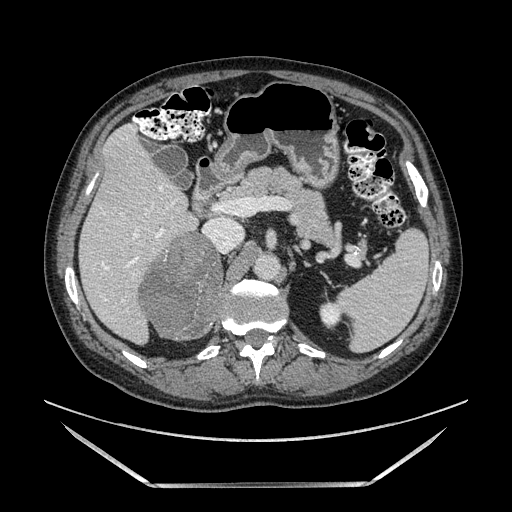
Contrast-enhanced abdominal CT, one axial slice; position 84 of 185 along the scan axis; soft-tissue window (W 400 / L 40 HU); 1.25 mm slice thickness; 512 × 512 image matrix. Male patient. Case-level facts recorded for this patient, not image findings: diagnosis: adrenocortical carcinoma; tumour side: right adrenal; tumour size at pathology: 10.3 cm; Ki-67 index: 20 %; stage (as recorded): 3.
Structures marked on this image (semi-automatically segmented with operator editing):
- mass: bounding box (x1, y1, x2, y2) in pixels: (143, 230, 222, 340)